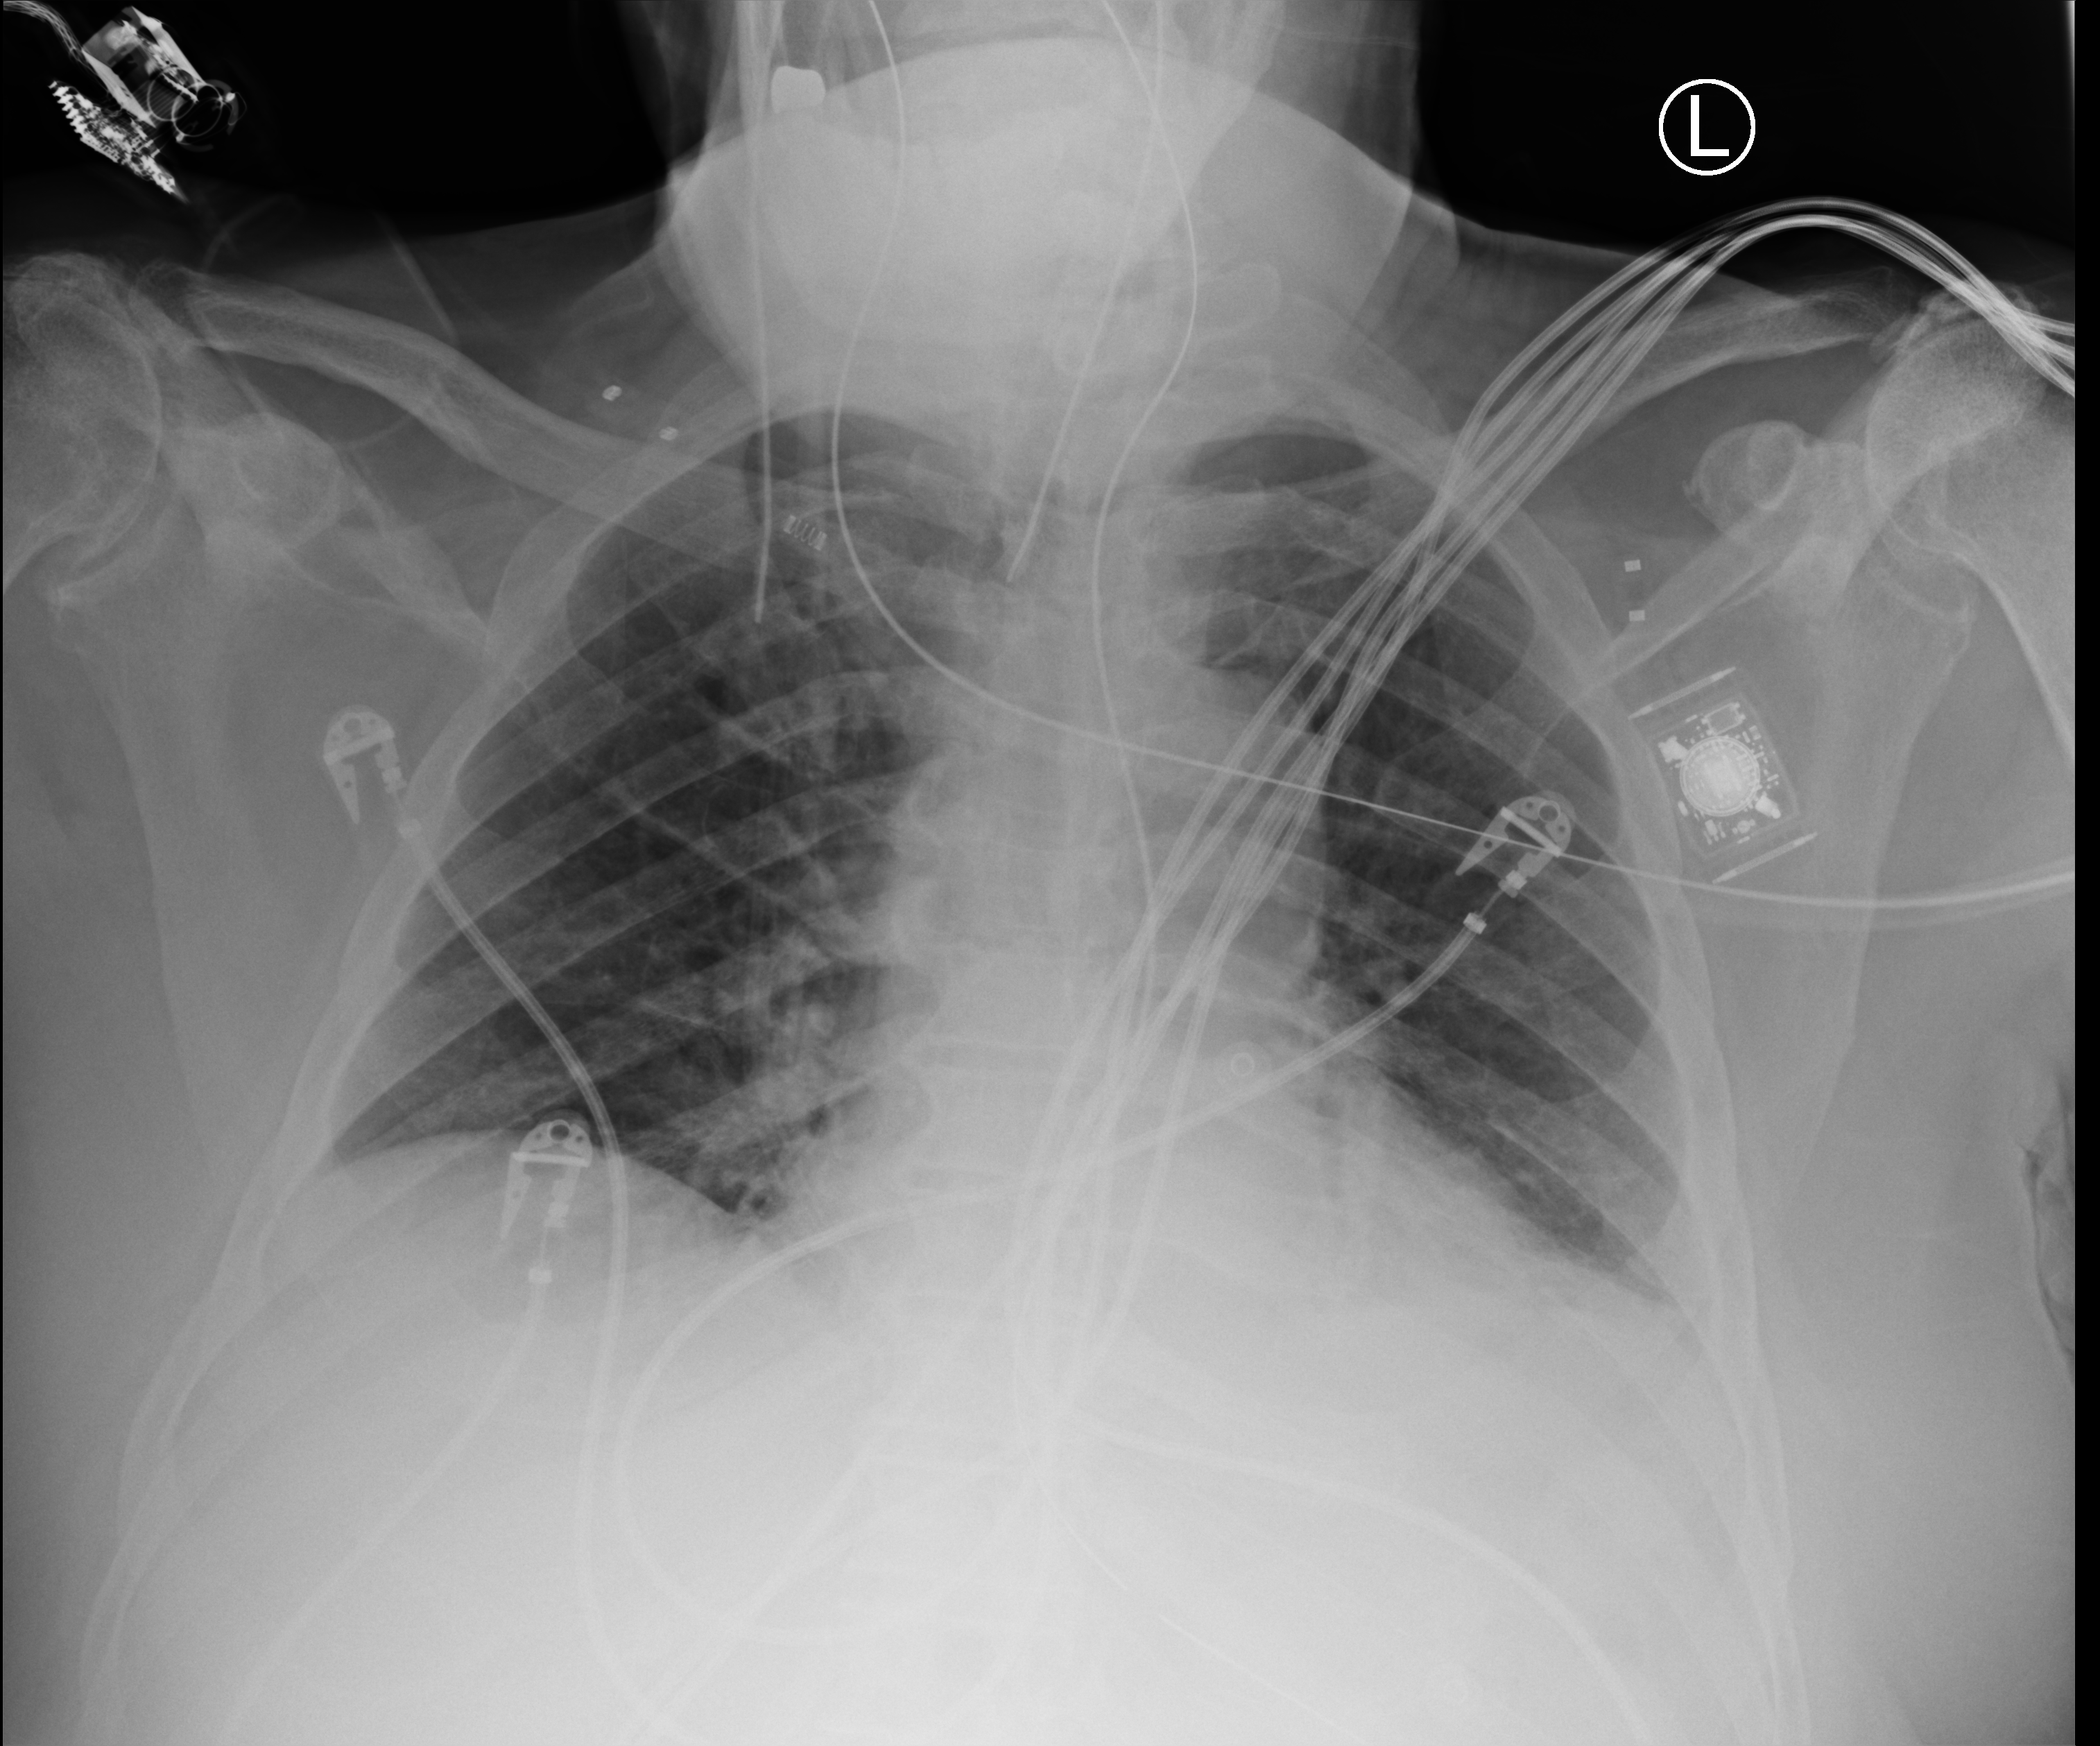
Bedside chest radiograph (computed radiography), anteroposterior (AP) projection. Patient hospitalised with COVID-19; male, aged 75–90 years.
Hospital-stay facts (about this admission, not read from this image; timing relative to this image not recorded): admitted to intensive care during this hospital stay: yes.